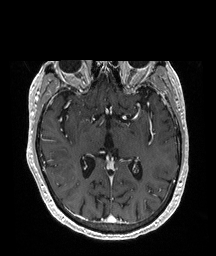
Brain MRI from a brain-tumour surgery series, one axial slice. T1-weighted post-contrast. 1 mm slice thickness. 216 × 256 image matrix, field of view 216 × 256 mm. Case-level facts recorded for this patient, not image findings: histopathology: Glioblastoma; WHO grade: 4; IDH mutation: no.
Structures marked on this image (manually delineated by an expert):
- tumour: bounding box <58,159,77,191> (left, top, right, bottom; pixels)